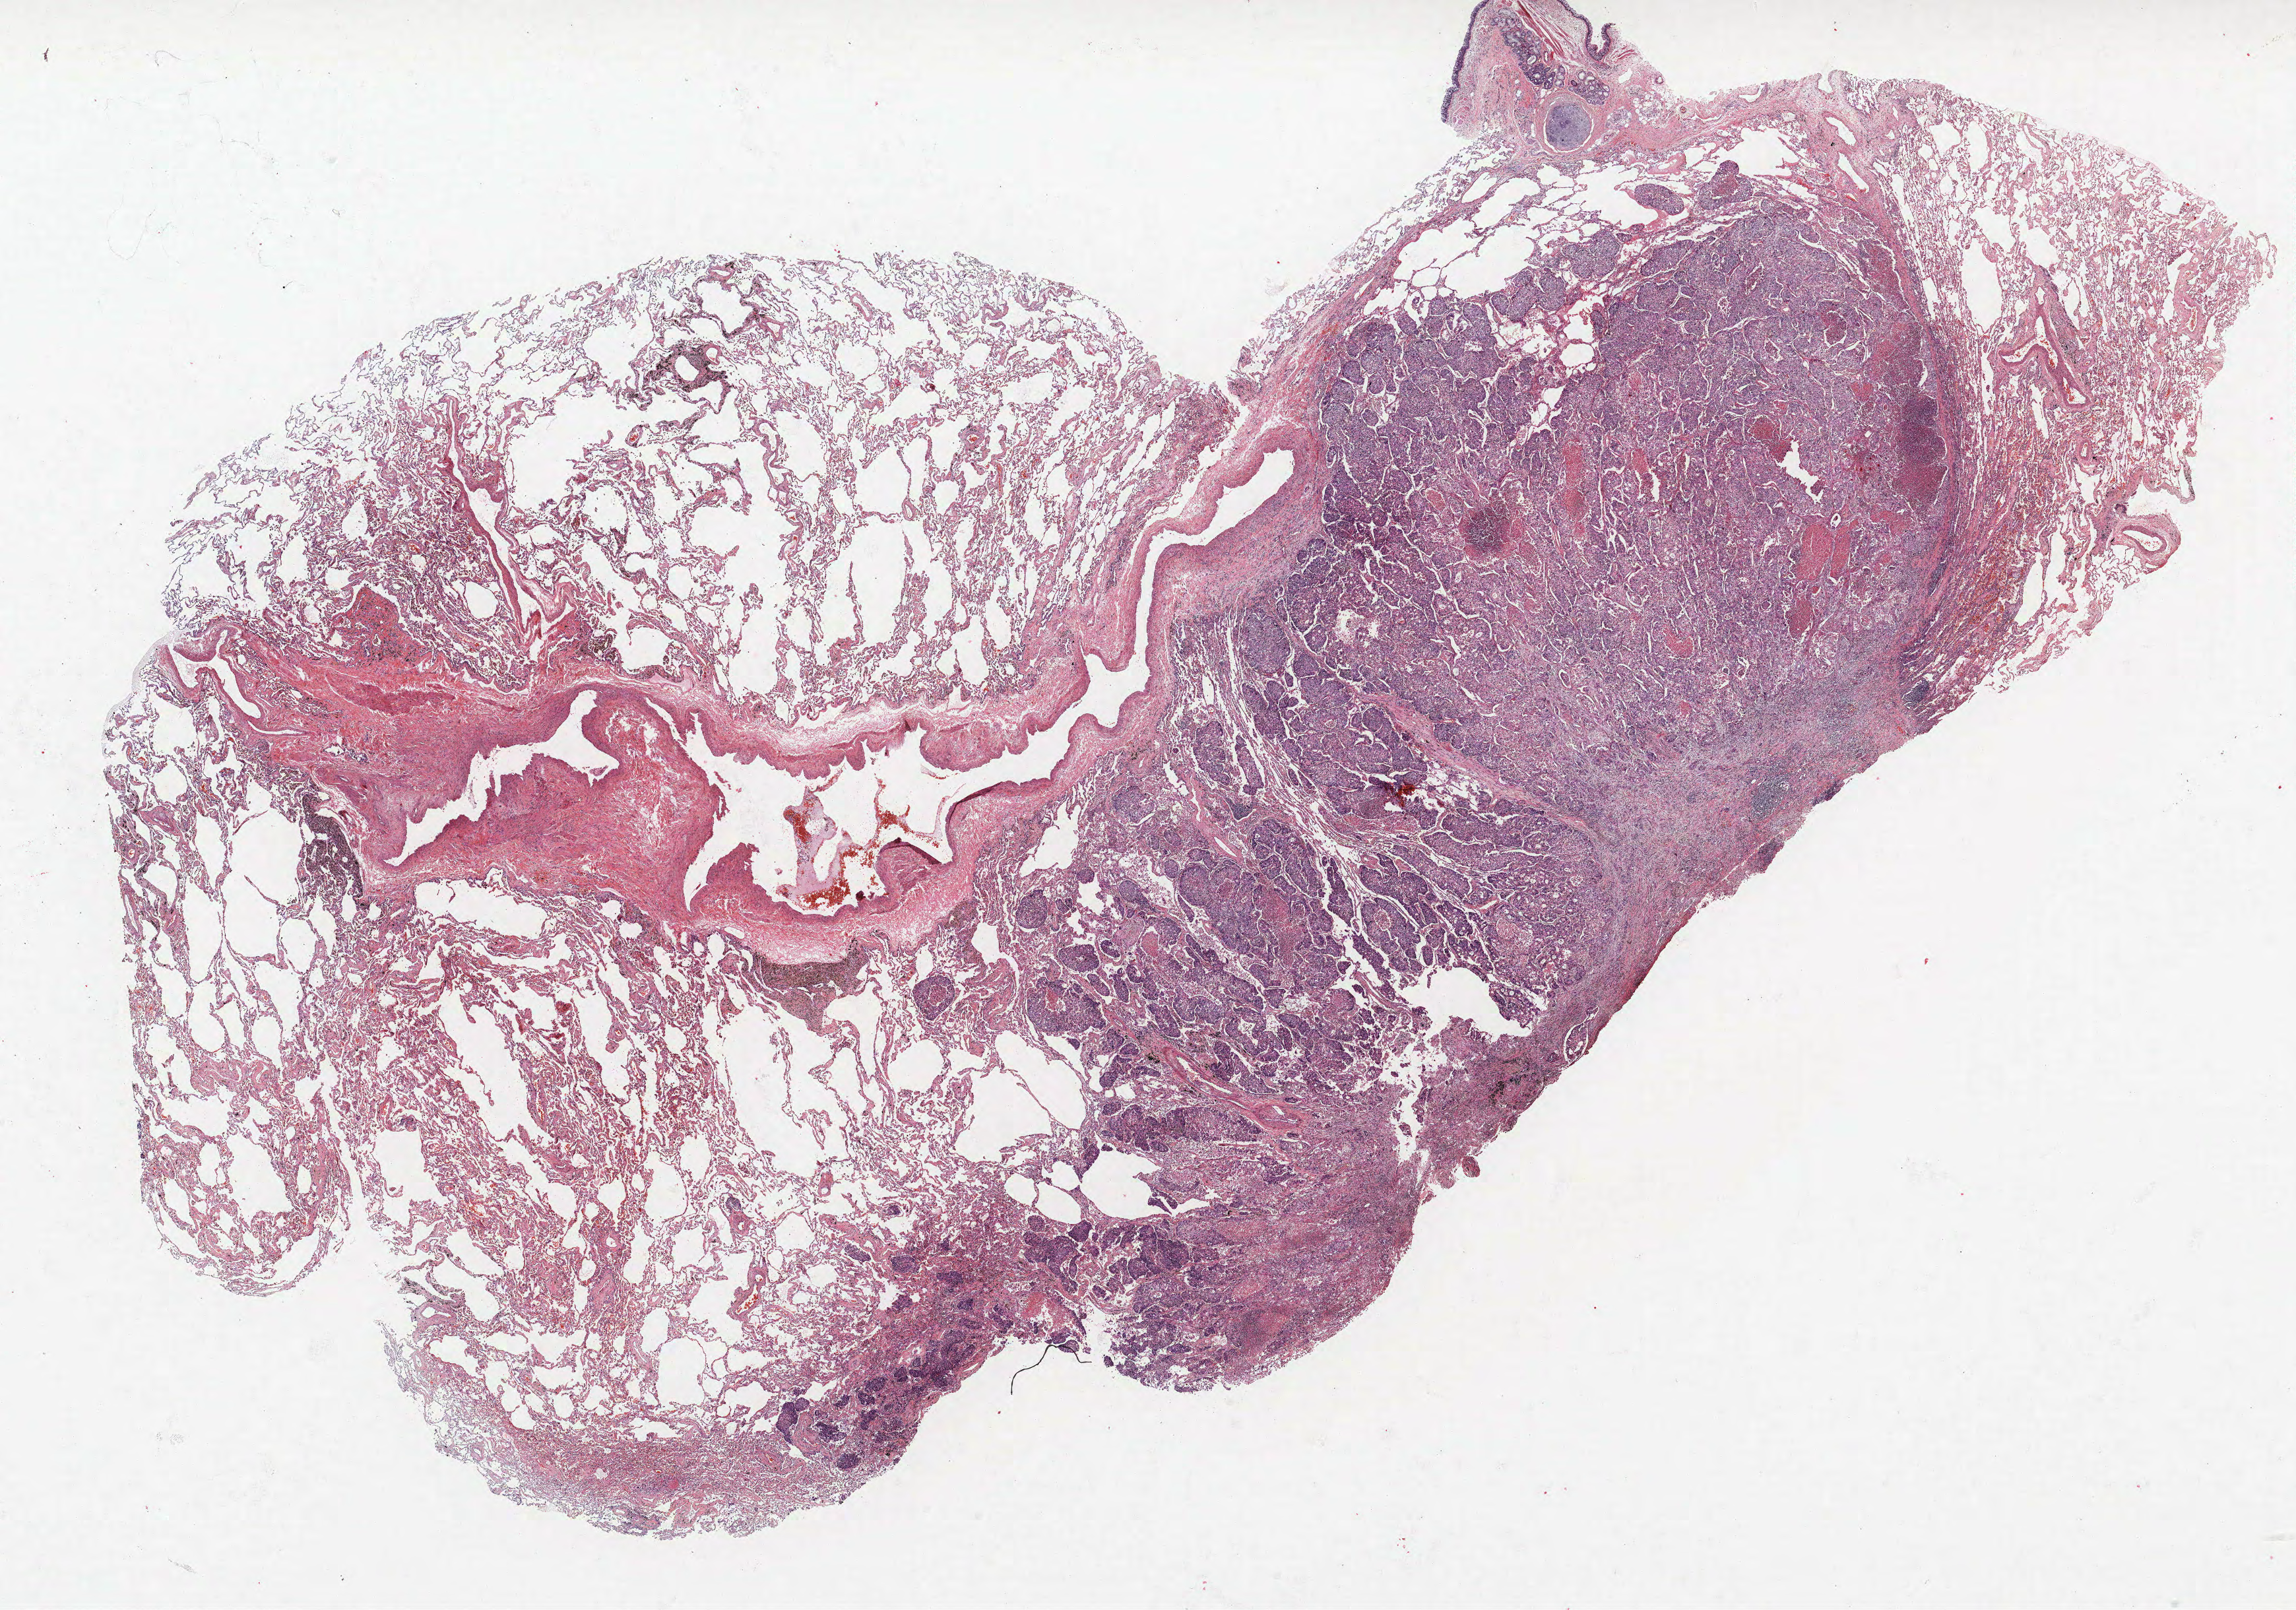
H&E-stained whole-slide image — a low-resolution overview of the entire scanned area, about 27.8 x 19.5 mm. Formalin-fixed paraffin-embedded (FFPE) section. Lung tissue. Male, age 60 at enrolment. Current smoker at enrolment. Grade: moderately differentiated (G2).
Tumour size (pathology): 35 mm. Primary tumour location (clinical record): left upper lobe. ICD-O-3 topography: upper lobe of lung (C34.1). Participant's lung-cancer diagnosis: Adenocarcinoma, NOS (ICD-O-3 8140/3). Stage (AJCC 6th edition): IB.